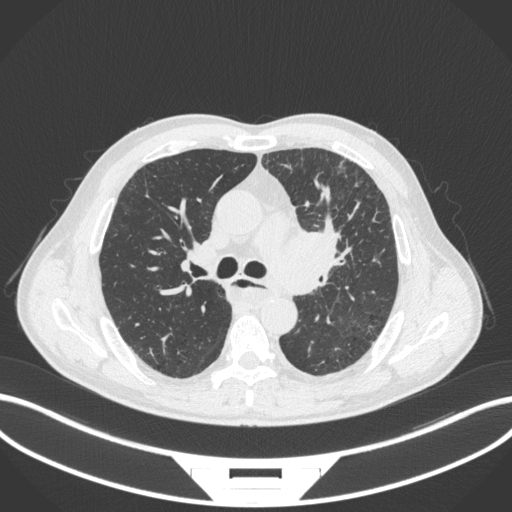
Chest CT, one axial slice; slice 243 of 411 in the series (ordered by position); lung window (W 1500 / L -600 HU); 1 mm slice thickness; 512 × 512 image matrix, field of view 400 × 400 mm. Male patient, age 57 years. Case-level facts recorded for this patient, not image findings: clinical TNM (as recorded): T2a N1 M0.
Outlined on this slice (bounding box drawn by a radiologist):
- lung tumour (recorded histology: squamous cell carcinoma): box from (x=265, y=221) to (x=344, y=301) px